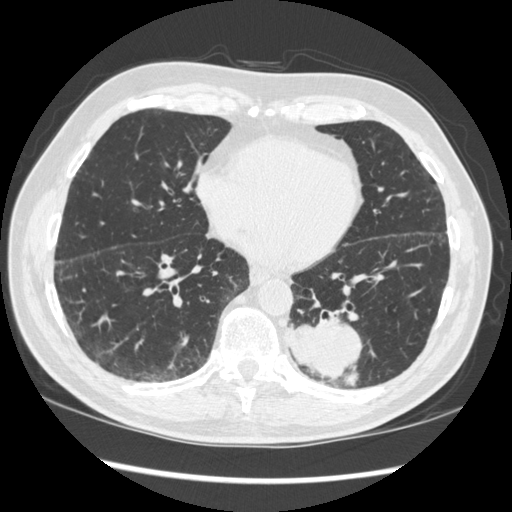
Low-dose screening chest CT, one axial slice. Slice 122 of 348 in the series (ordered by position). Lung window (W 1500 / L -600 HU). 512 × 512 image matrix, field of view 360 × 360 mm.
Structures marked on this image (expert manual segmentation):
- lesion 1 (tumor, lower lobe of left lung): bounding box (x1, y1, x2, y2) in pixels: (288, 315, 361, 383)